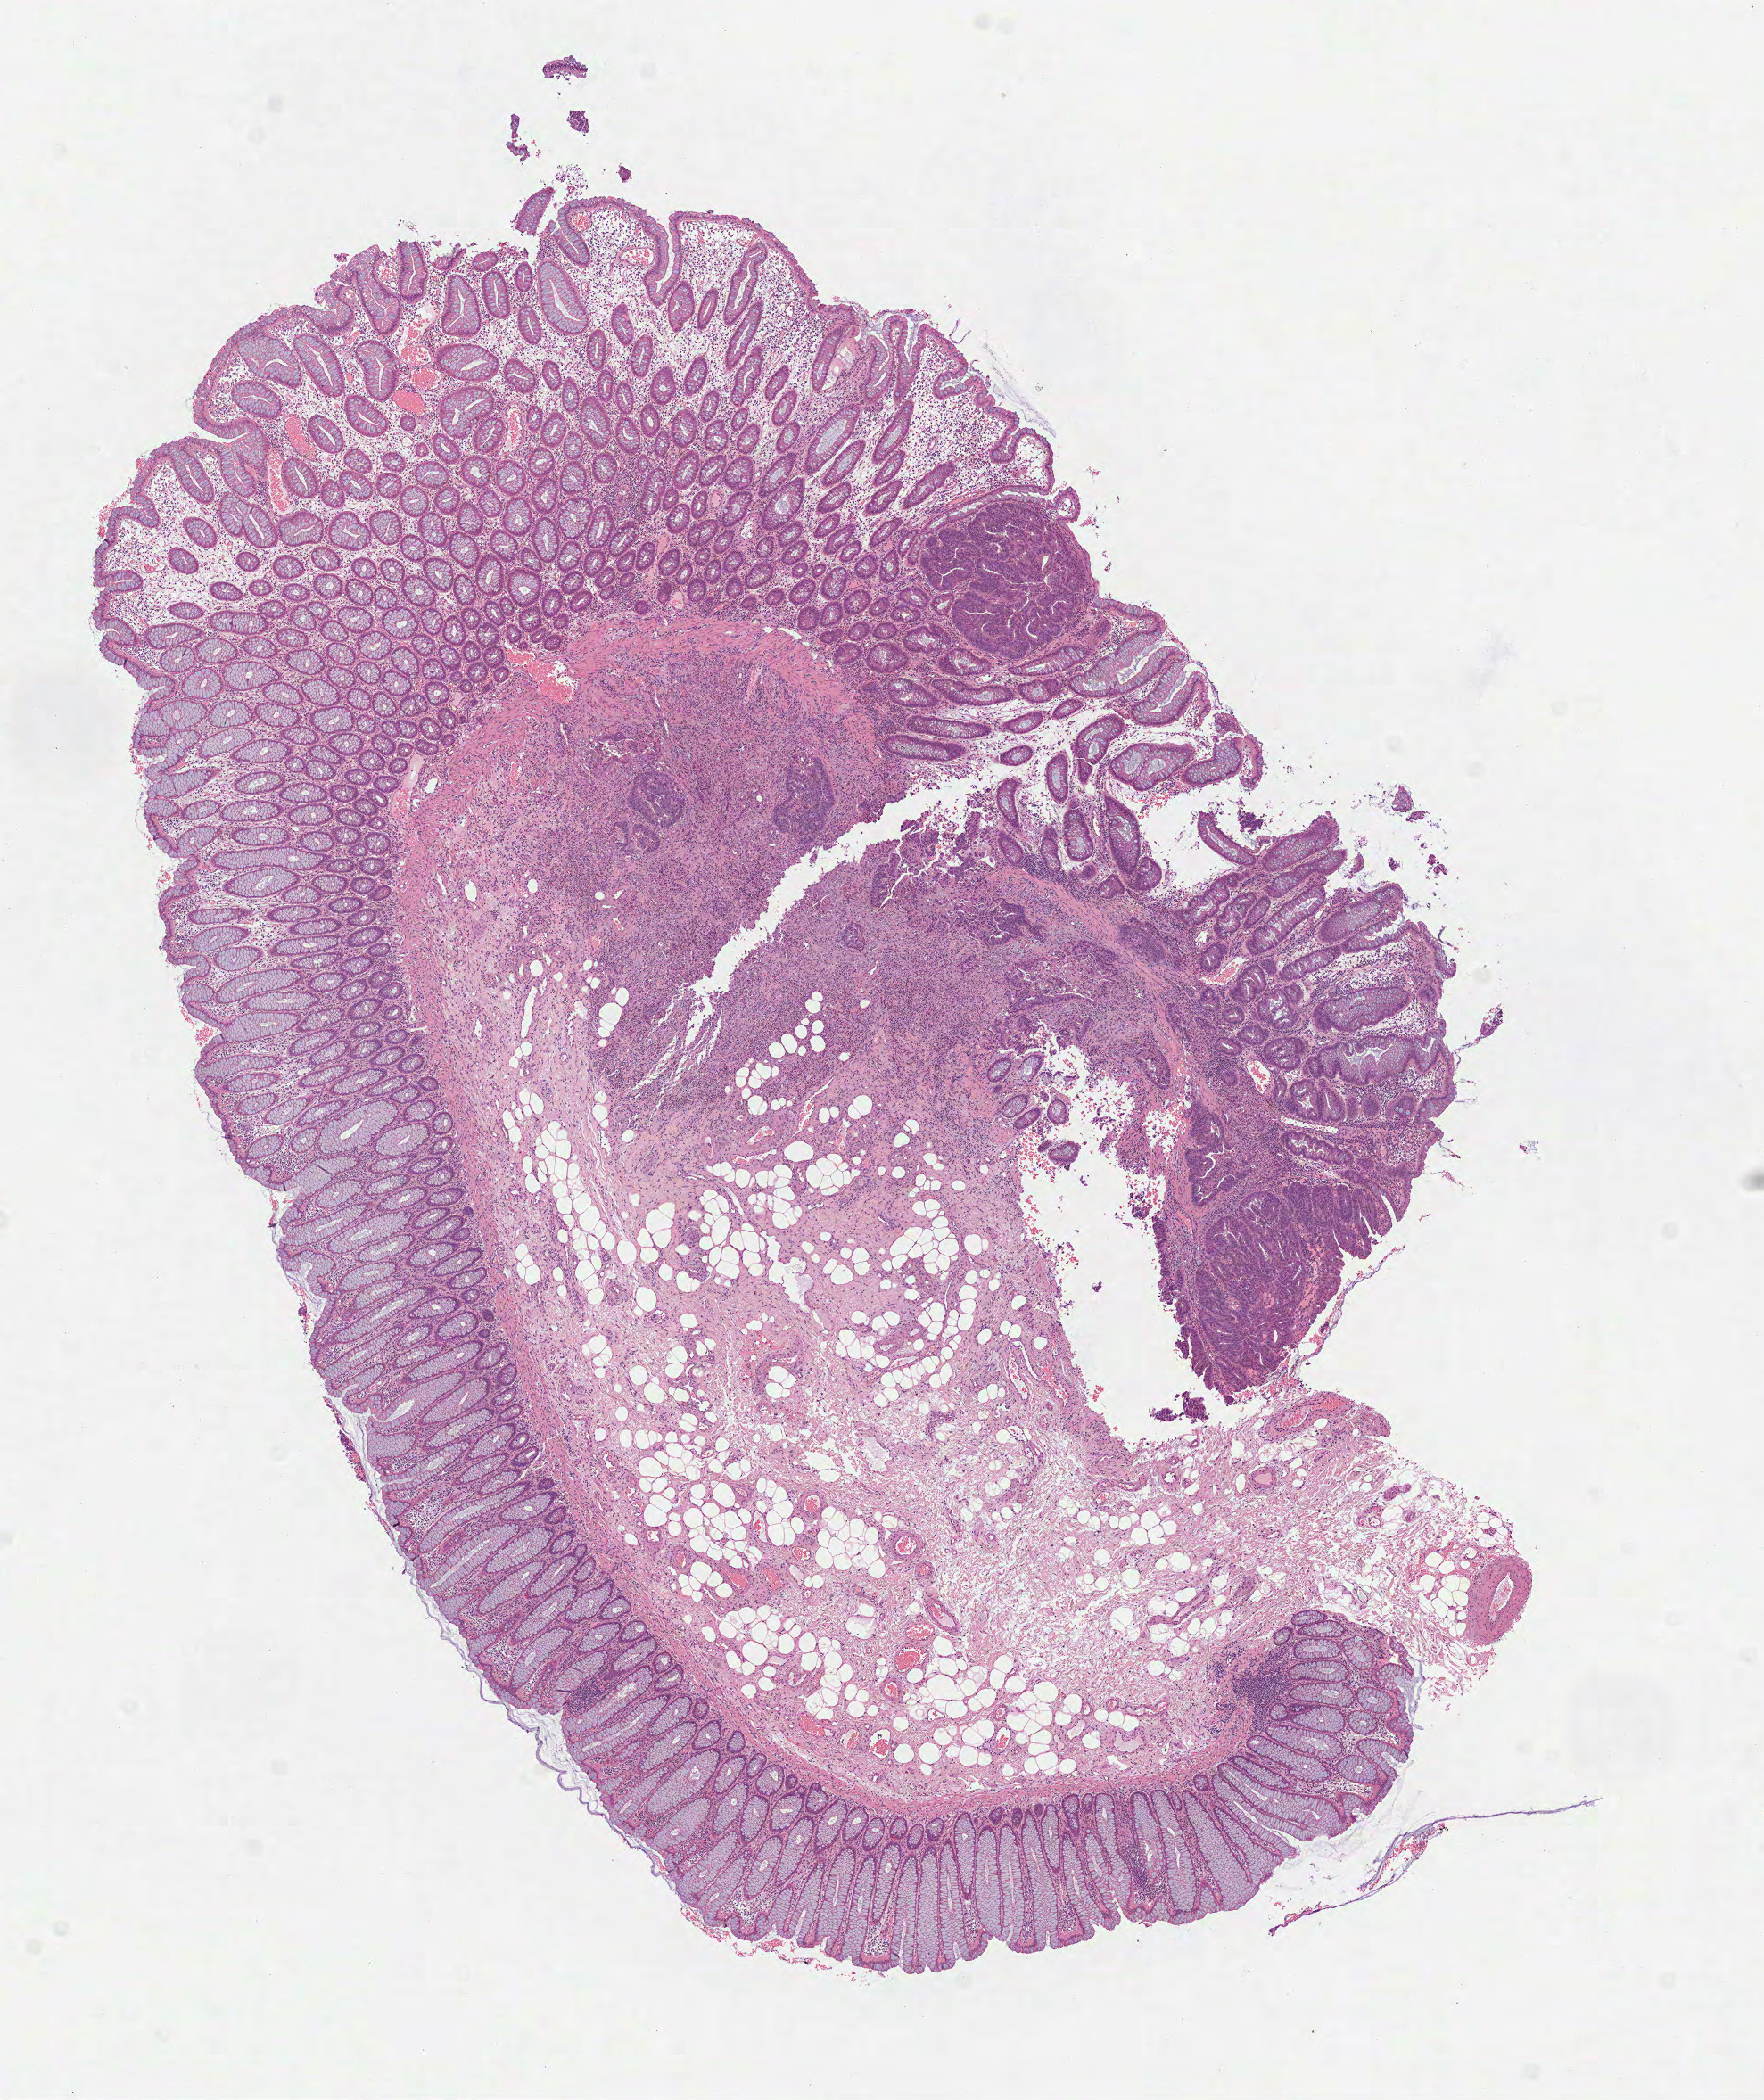
Whole-slide histology image, Hematoxylin and eosin (H&E) stained — low-resolution overview of the scanned area, about 8.0 x 9.5 mm (acquisition: 40x scan); formalin-fixed paraffin-embedded (FFPE) diagnostic section; primary tumour sample from the rectum. Male patient; age at initial diagnosis 73 years.
Histologic diagnosis: Adenocarcinoma, NOS.